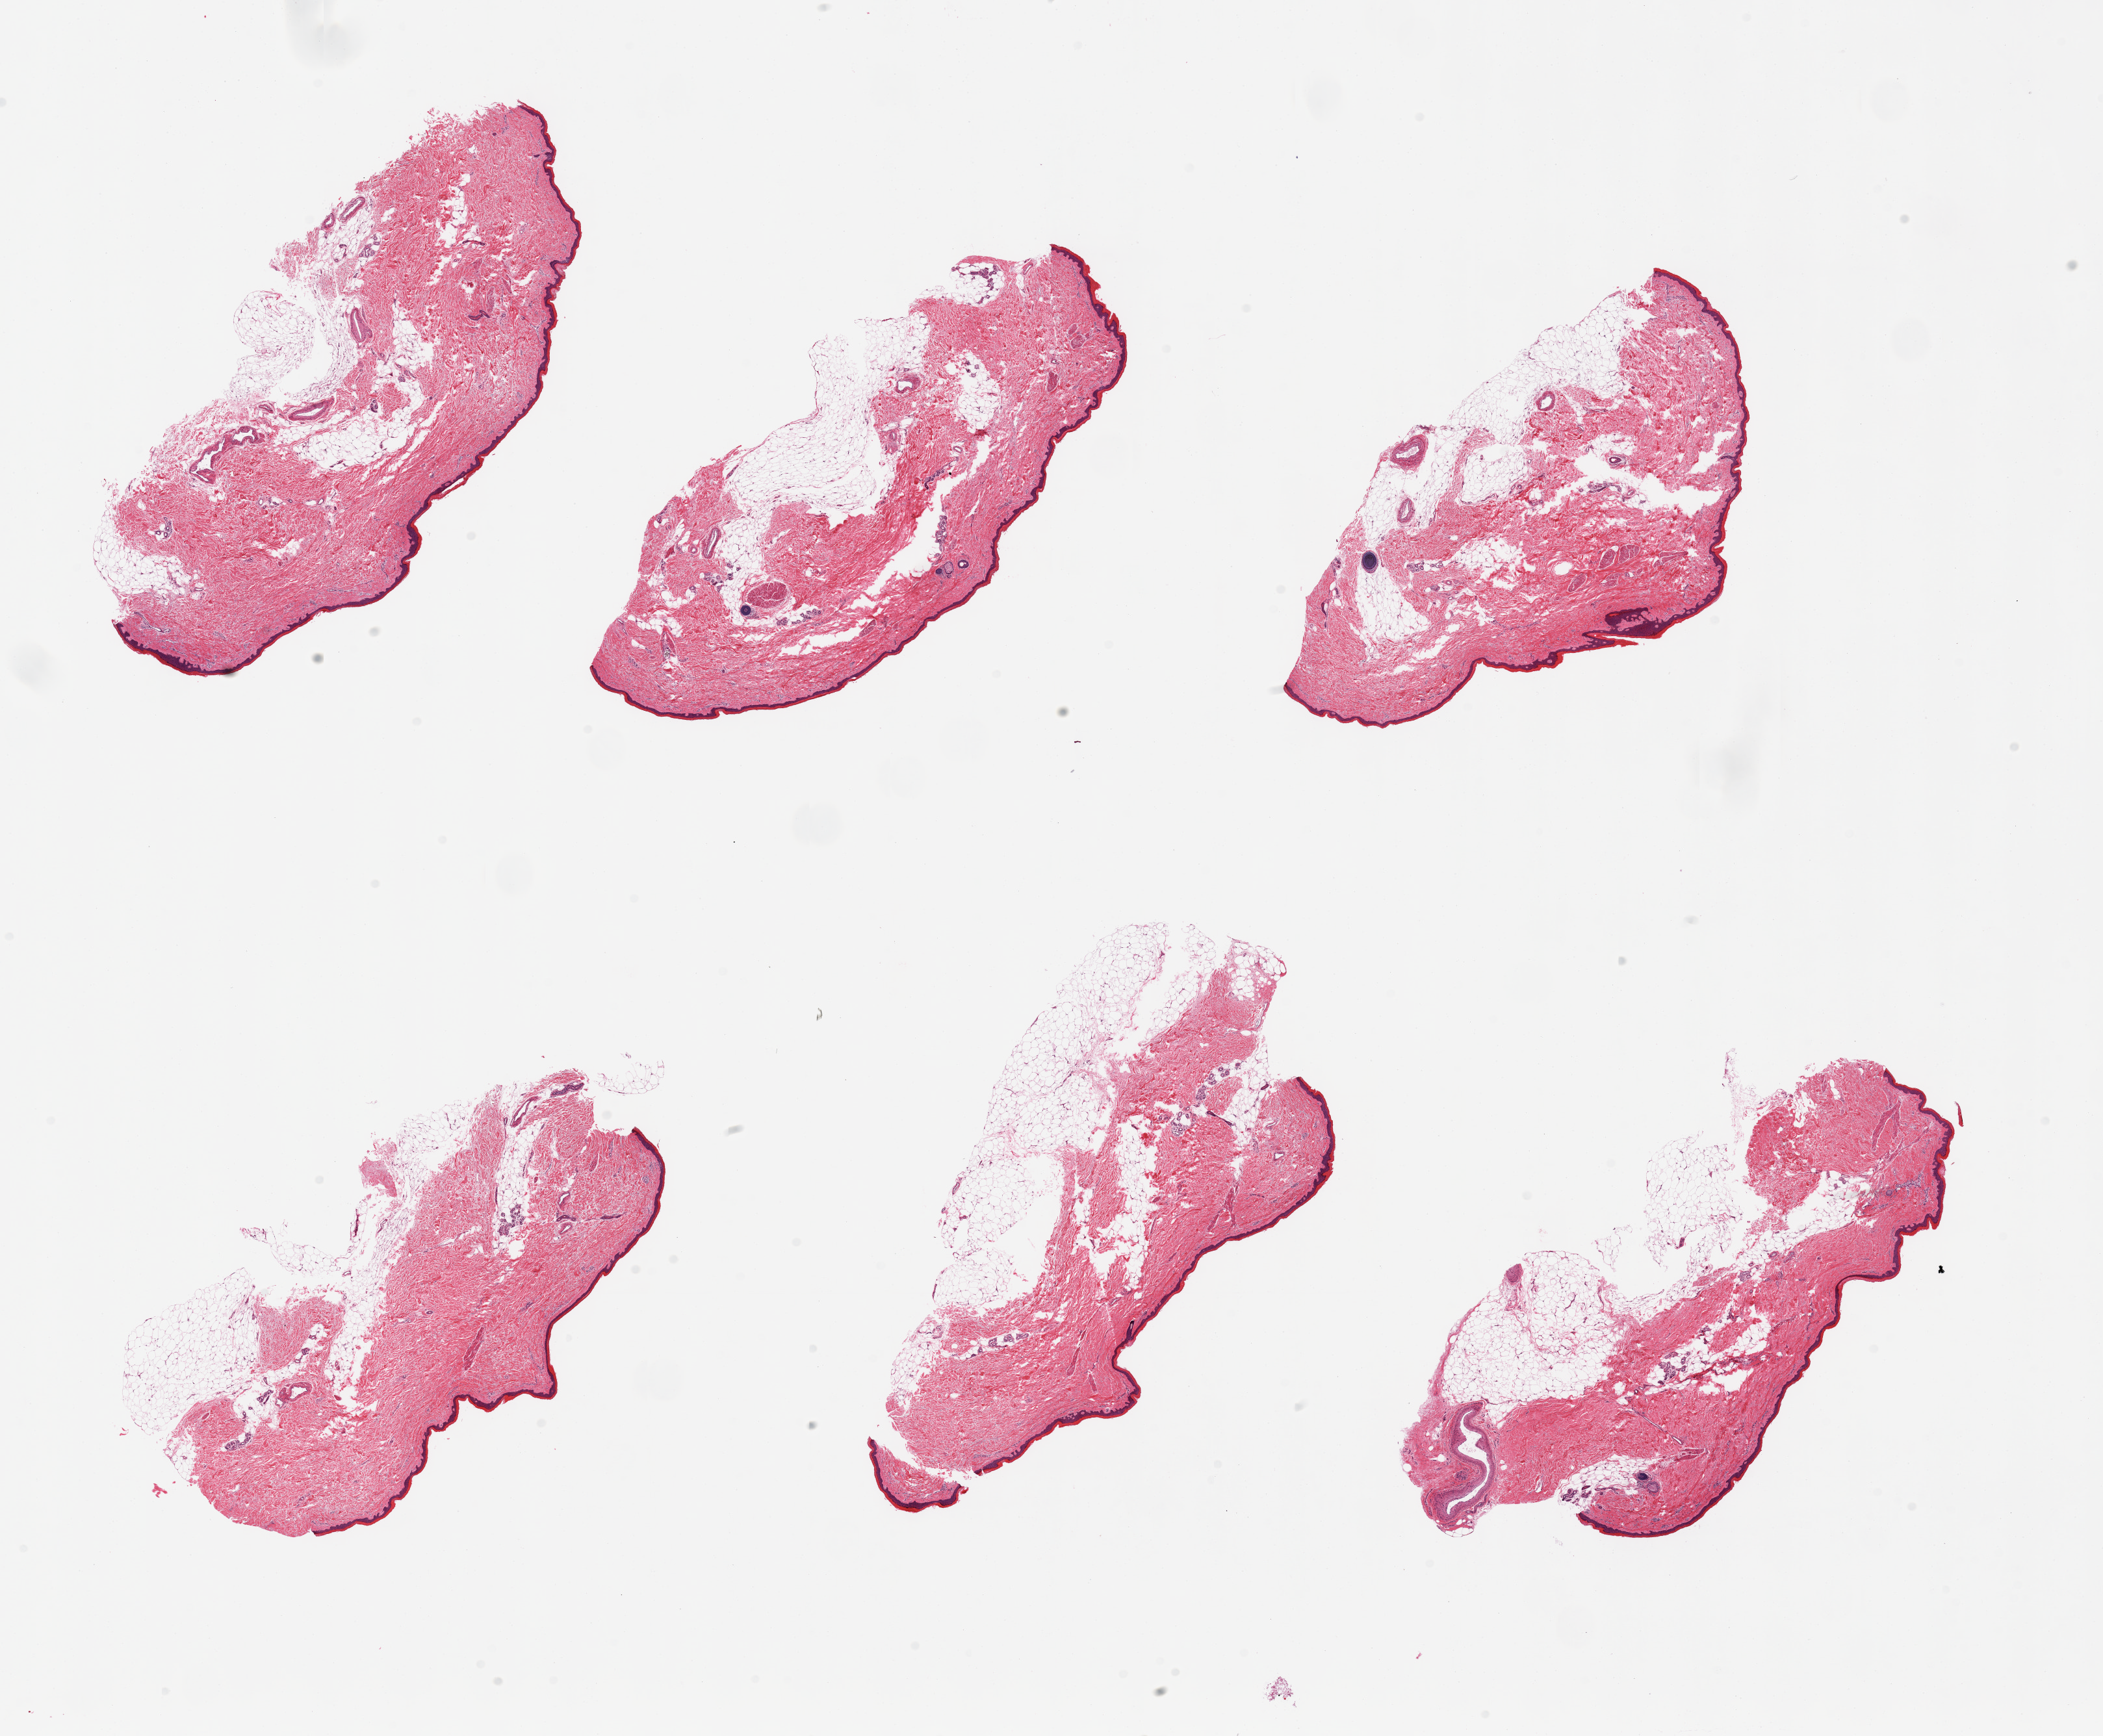
Hematoxylin and eosin (H&E) whole-slide image — a low-resolution overview of the entire scanned area, about 25.6 x 21.1 mm (from a 20x scan). PAXgene-fixed paraffin-embedded (PFPE) section. Section of skin of lower leg (target tissue). Donor tissue sample. Female donor.
• review note (as recorded): 6 pieces, all contain residual attached adipose tissue from 10-30%, squamous epithelium measures 30-40 microns